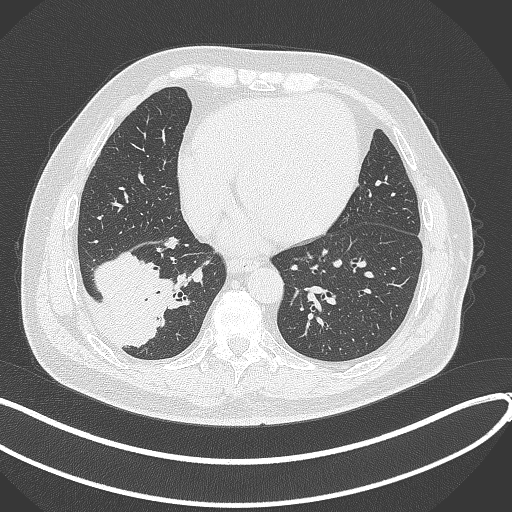
Chest CT, one axial slice; position 120 of 360 along the scan axis; reconstruction kernel B70f; 120 kVp; lung window (W 1500 / L -600 HU); 1 mm slice thickness; 512 × 512 image matrix, field of view 400 × 400 mm. Male patient, age 59 years.
Annotated regions visible in this slice (bounding box drawn by a radiologist):
- lung tumour (recorded histology: adenocarcinoma): bounding box <91,244,178,351> (left, top, right, bottom; pixels)